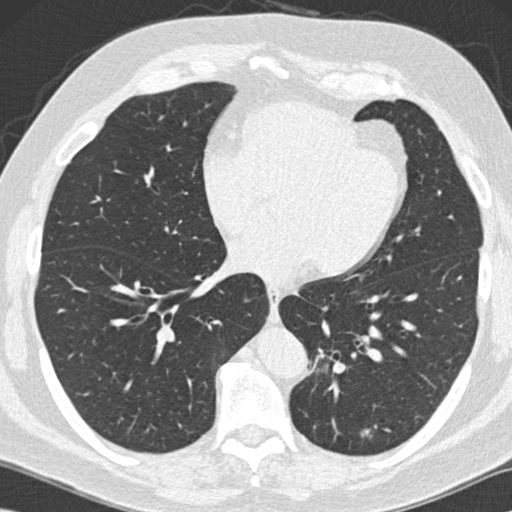
Low-dose screening chest CT, one axial slice; reconstruction kernel B30f; 120 kVp; lung window (W 1500 / L -600 HU); 2 mm slice thickness; 512 × 512 image matrix.
Structures marked on this image (expert manual segmentation):
- lesion 1 (tumor, lower lobe of left lung): bounding box (x1, y1, x2, y2) in pixels: (361, 429, 370, 436)